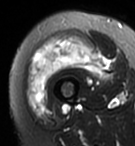
MRI of an extremity soft-tissue mass, one axial slice. Slice 28 of 95 in the series (ordered by position). T2-weighted fat-saturated. MR volume resampled by the dataset authors to the PET/CT grid (not the native acquisition matrix). 135 × 146 image matrix, field of view 132 × 143 mm. Female patient. Case-level facts recorded for this patient, not image findings: histological type: pleiomorphic undifferentiated sarcoma; grade: high; site of the primary tumour: right quadricep.
Structures marked on this image (expert contour drawn on MRI and transferred to this co-registered scan by the dataset authors):
- gross tumour volume including surrounding oedema: bounding box [x1, y1, x2, y2] px = [28, 36, 106, 114]
- gross tumour volume (mass): [39, 38, 104, 64]